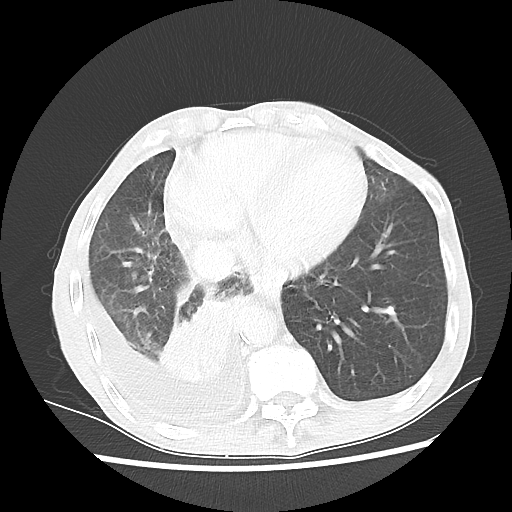
Chest CT, one axial slice. Slice 18 of 60 in the series (ordered by position). 80 kVp. Lung window (W 1500 / L -600 HU). 5 mm slice thickness. 512 × 512 image matrix. Patient: male, 76 years. From the clinical record (not read from this slice): clinical TNM (as recorded): T3 N3 M1a; histopathological grade: G3.
Structures marked on this image (rectangle marked by the reading radiologist):
- lung tumour (recorded histology: squamous cell carcinoma): bounding box <154,288,240,389> (left, top, right, bottom; pixels)